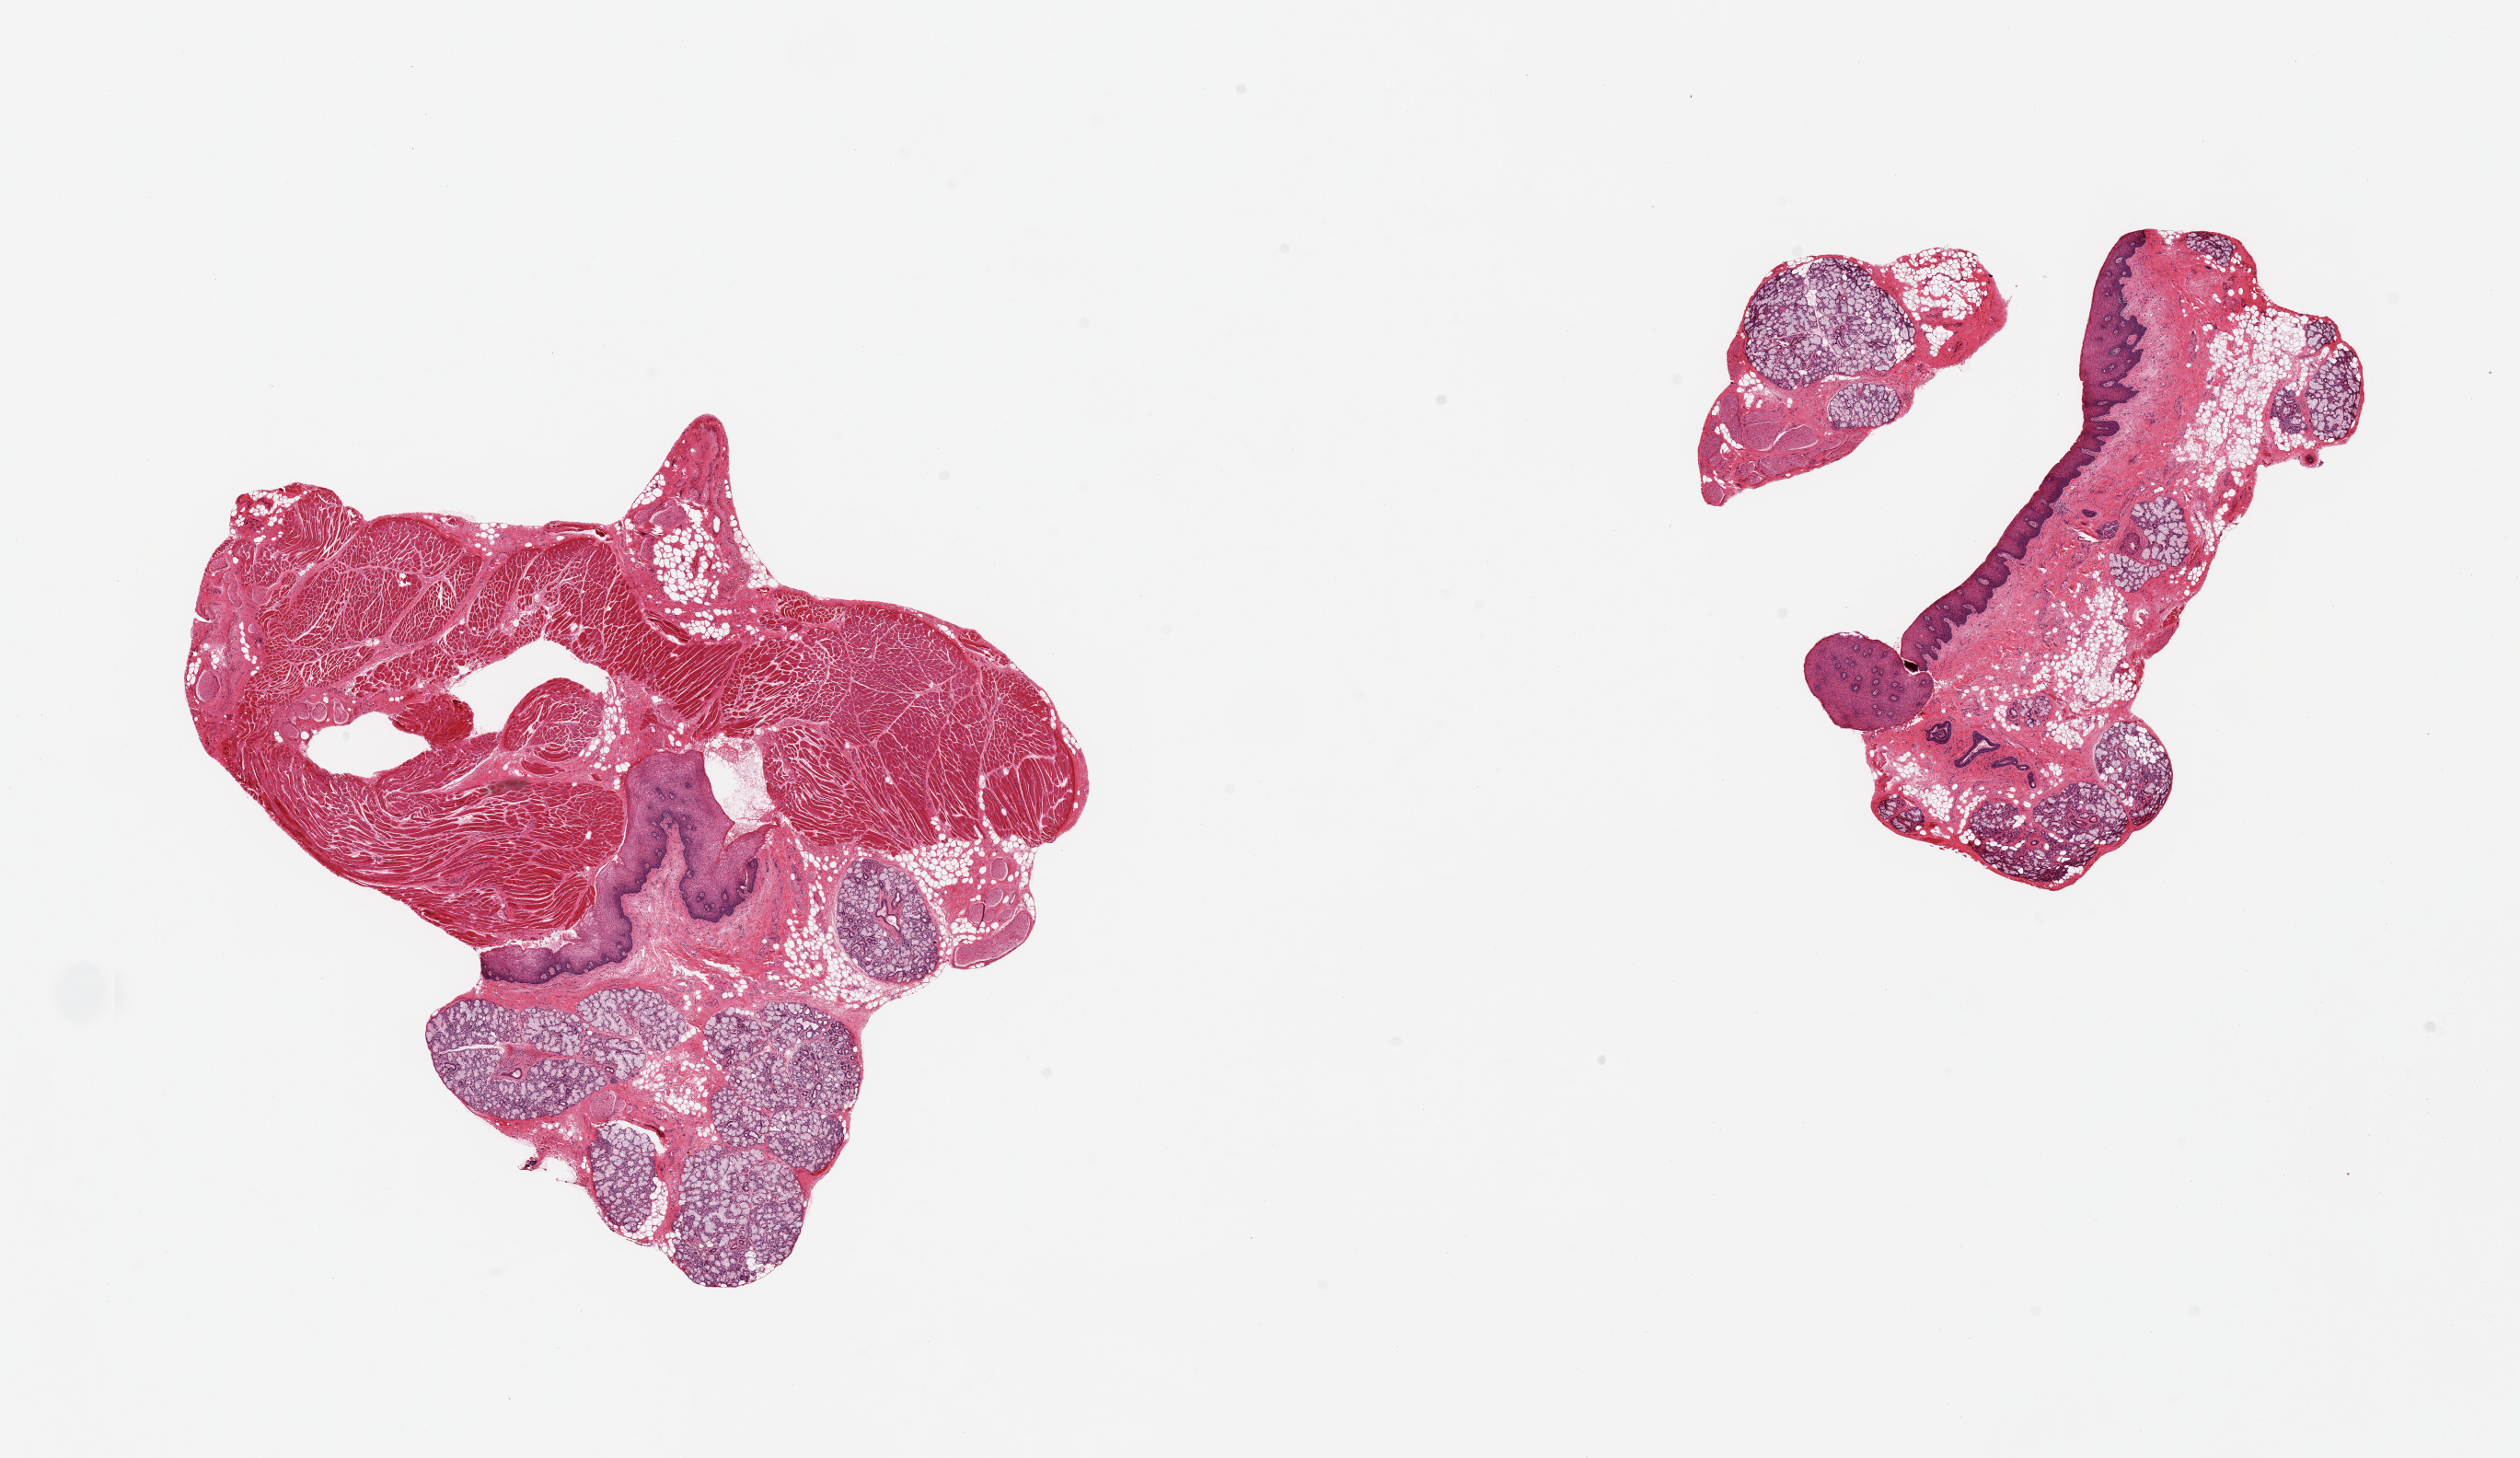
H&E whole-slide image — a low-resolution overview of the entire scanned area, about 21.7 x 12.5 mm.
* specimen: PAXgene-fixed, paraffin-embedded tissue; section of minor salivary gland (target tissue); donor tissue sample